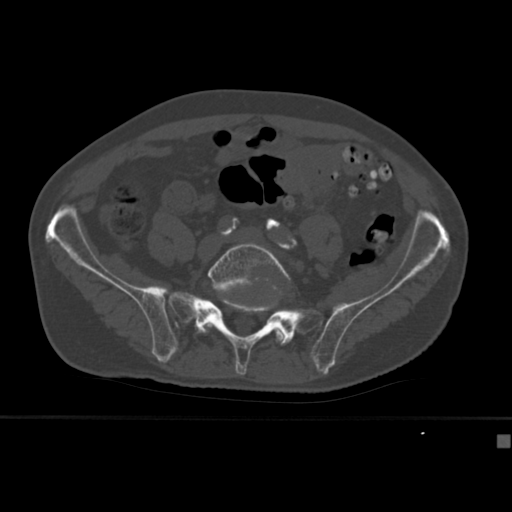
CT including the spine, one axial slice; reconstruction kernel Br40s; 120 kVp; bone window (W 1800 / L 400 HU); 1.5 mm slice thickness; 512 × 512 image matrix. Male patient, age 64 years. Case-level facts recorded for this patient, not image findings: primary cancer: uterus; vertebrae with lytic lesions (as recorded): T1, T4, T5, T7, L5.
Outlined on this slice (semi-automatically segmented with operator editing):
- L5 vertebra: box from (x=198, y=242) to (x=290, y=346) px